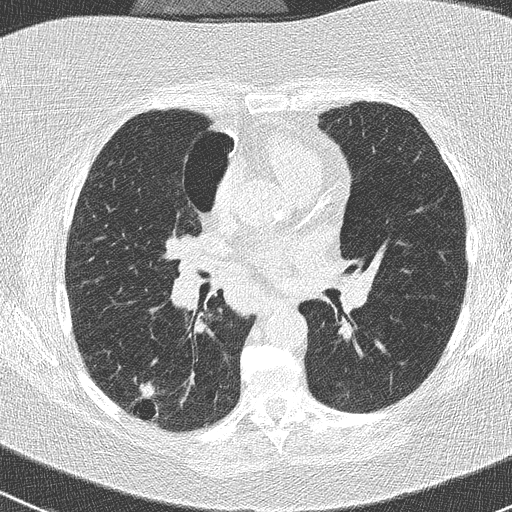
Low-dose screening chest CT, one axial slice; slice 139 of 261 in the series (ordered by position); 120 kVp; lung window (W 1500 / L -600 HU); 2 mm slice thickness; 512 × 512 image matrix.
Structures marked on this image (outlined manually by an expert reader):
- lesion 1 (tumor, lower lobe of right lung): bounding box (x1, y1, x2, y2) in pixels: (139, 382, 156, 399)